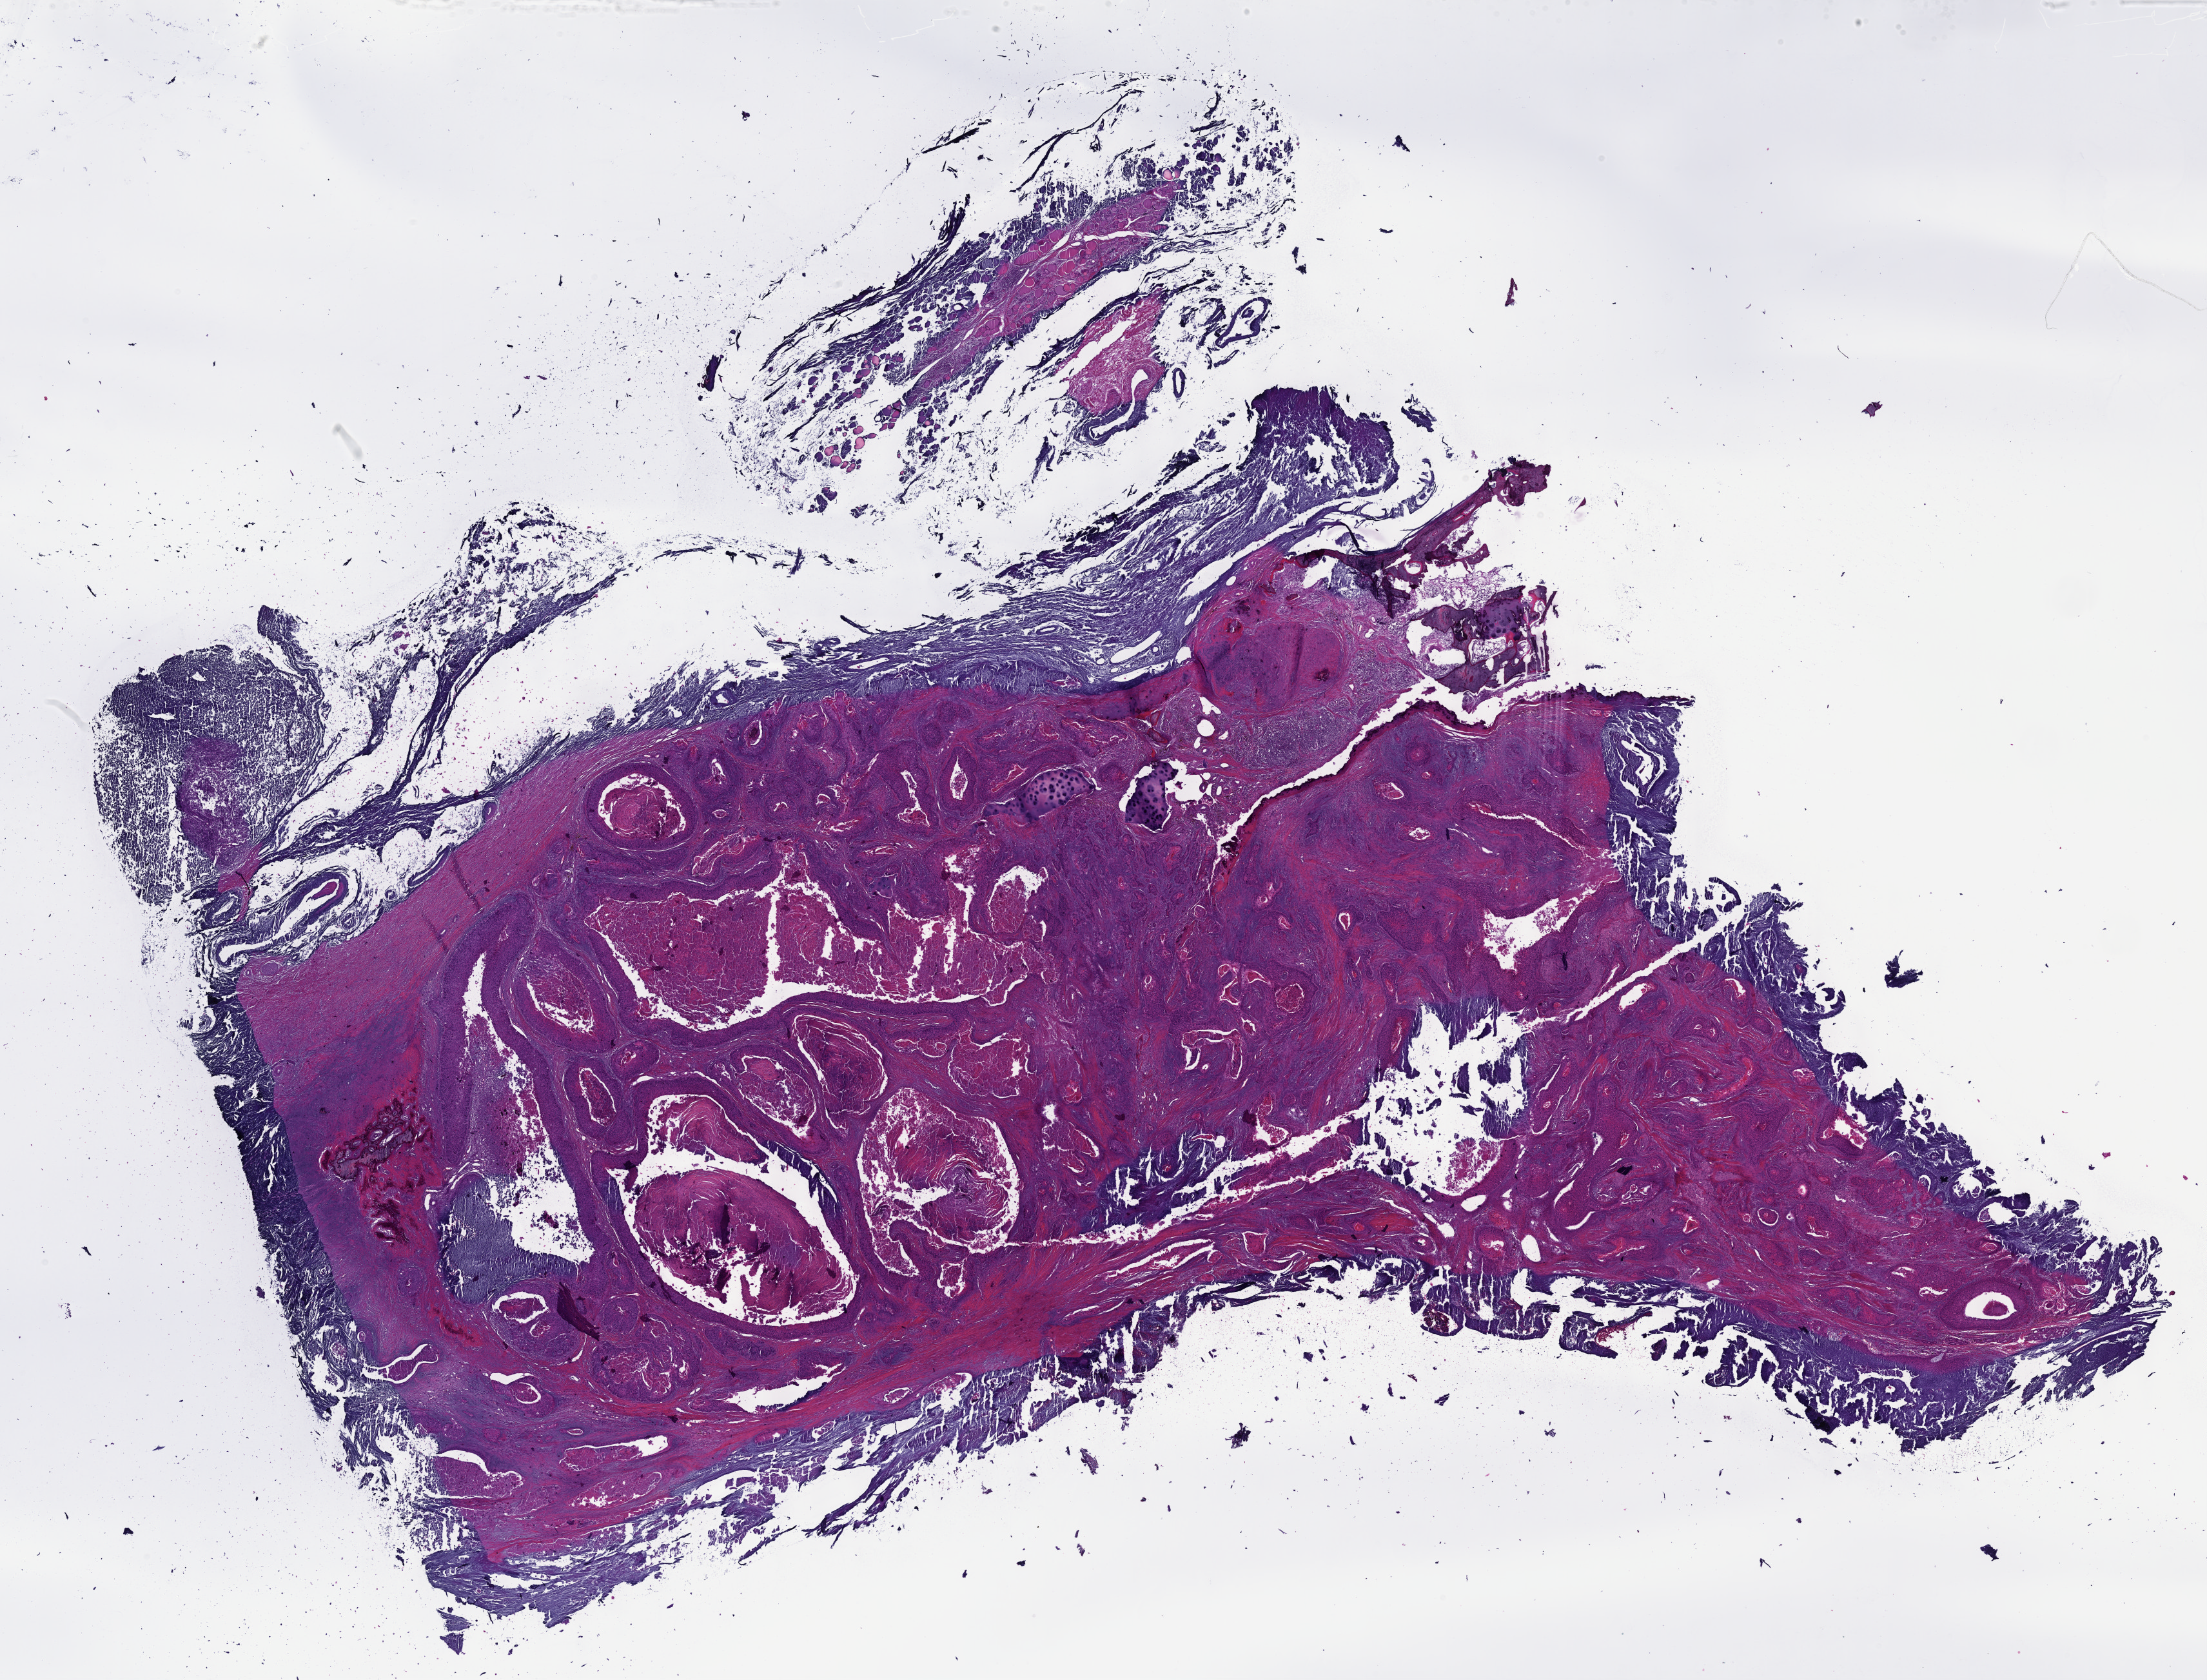
Digitized Hematoxylin and eosin (H&E) stained tissue section (whole slide), a low-resolution overview of the entire scanned area, about 27.7 x 21.1 mm (from a 40x scan); formalin-fixed paraffin-embedded (FFPE) diagnostic section; sample: primary tumour, head and neck. Male patient; age at initial diagnosis 76 years. Histologic grade: G2 (moderately differentiated).
AJCC pathologic stage: IVA. Diagnosis: Squamous cell carcinoma, NOS. Laterality: midline.